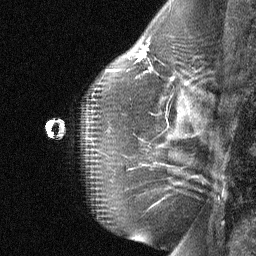
Breast MRI (dynamic contrast-enhanced), one sagittal slice; slice 42 of 64 in the series (ordered by position); dynamic contrast-enhanced study with each time point stored as its own series, time point 2 of 3 at this slice position (early post-contrast, ordered by acquisition time); 1.5 T; TE 4.8 ms, TR 27 ms; 2 mm slice thickness; 256 × 256 image matrix. Patient: female, 51 years. Case-level facts recorded for this patient, not image findings: setting: breast cancer imaged before/during neoadjuvant chemotherapy; receptor status: HR-positive, HER2-negative.
Structures marked on this image (semi-automatic segmentation, software-assisted and operator-edited):
- analysis volume of interest (the breast-tissue region the enhancement analysis was run in; not a lesion): box from (x=87, y=35) to (x=179, y=103) px
- tumour enhancement mask (voxels above the 90 % enhancement threshold inside the analysis volume of interest): (x=139, y=51)–(x=146, y=58)